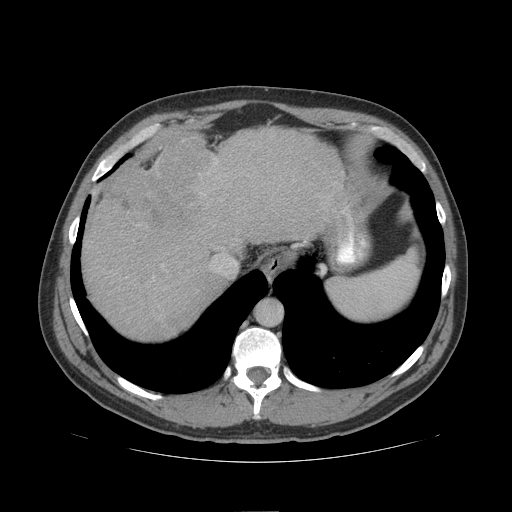
Contrast-enhanced abdominal CT (liver protocol), one axial slice; position 84 of 109 along the scan axis; reconstruction kernel STANDARD; soft-tissue window (W 400 / L 40 HU); 2.5 mm slice thickness; 512 × 512 image matrix. From the clinical record (not read from this slice): diagnosis: hepatocellular carcinoma (patient treated with transarterial chemoembolisation; whether this scan precedes or follows treatment is not stated here); TNM stage (as recorded): Stage-IIIB; Child-Pugh class: A; tumour differentiation: poorly differentiated; tumour nodularity: multinodular.
Structures marked on this image (semi-automatically segmented with operator editing):
- abdominal aorta: bounding box [x1, y1, x2, y2] px = [258, 301, 281, 326]
- liver parenchyma outside the tumour (the mass and vessels are separate outlines, so this box may not span the whole liver): [82, 126, 352, 338]
- mass: [112, 140, 209, 230]